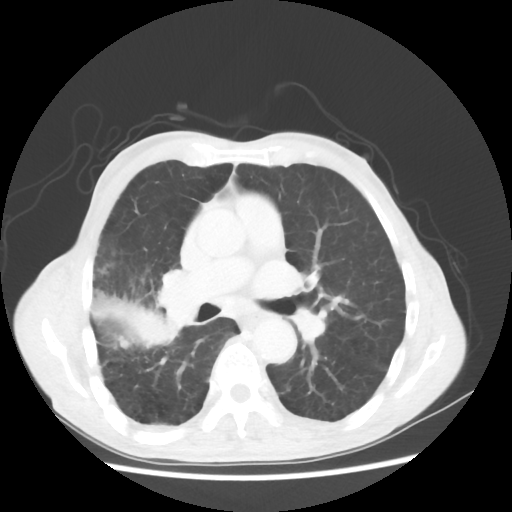
Chest CT, one axial slice. Position 29 of 58 along the scan axis. Reconstruction kernel STANDARD. Lung window (W 1500 / L -600 HU). 512 × 512 image matrix. Male patient, age 75 years. Case-level facts recorded for this patient, not image findings: clinical TNM (as recorded): T4 N1 M1.
Outlined on this slice (bounding box drawn by a radiologist):
- lung tumour (recorded histology: adenocarcinoma): box from (x=80, y=279) to (x=182, y=357) px